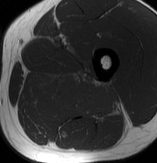
MRI of an extremity soft-tissue mass, one axial slice. Slice 44 of 70 in the series (ordered by position). MR volume resampled by the dataset authors to the PET/CT grid (not the native acquisition matrix). 3.27 mm slice thickness. 157 × 163 image matrix, field of view 153 × 159 mm. Male patient. Case-level facts recorded for this patient, not image findings: histological type: extraskeletal osteosarcoma; grade: high; site of the primary tumour: left adductur.
Outlined on this slice (expert contour drawn on MRI and transferred to this co-registered scan by the dataset authors):
- gross tumour volume (mass): bounding box (x1, y1, x2, y2) in pixels: (26, 72, 123, 123)